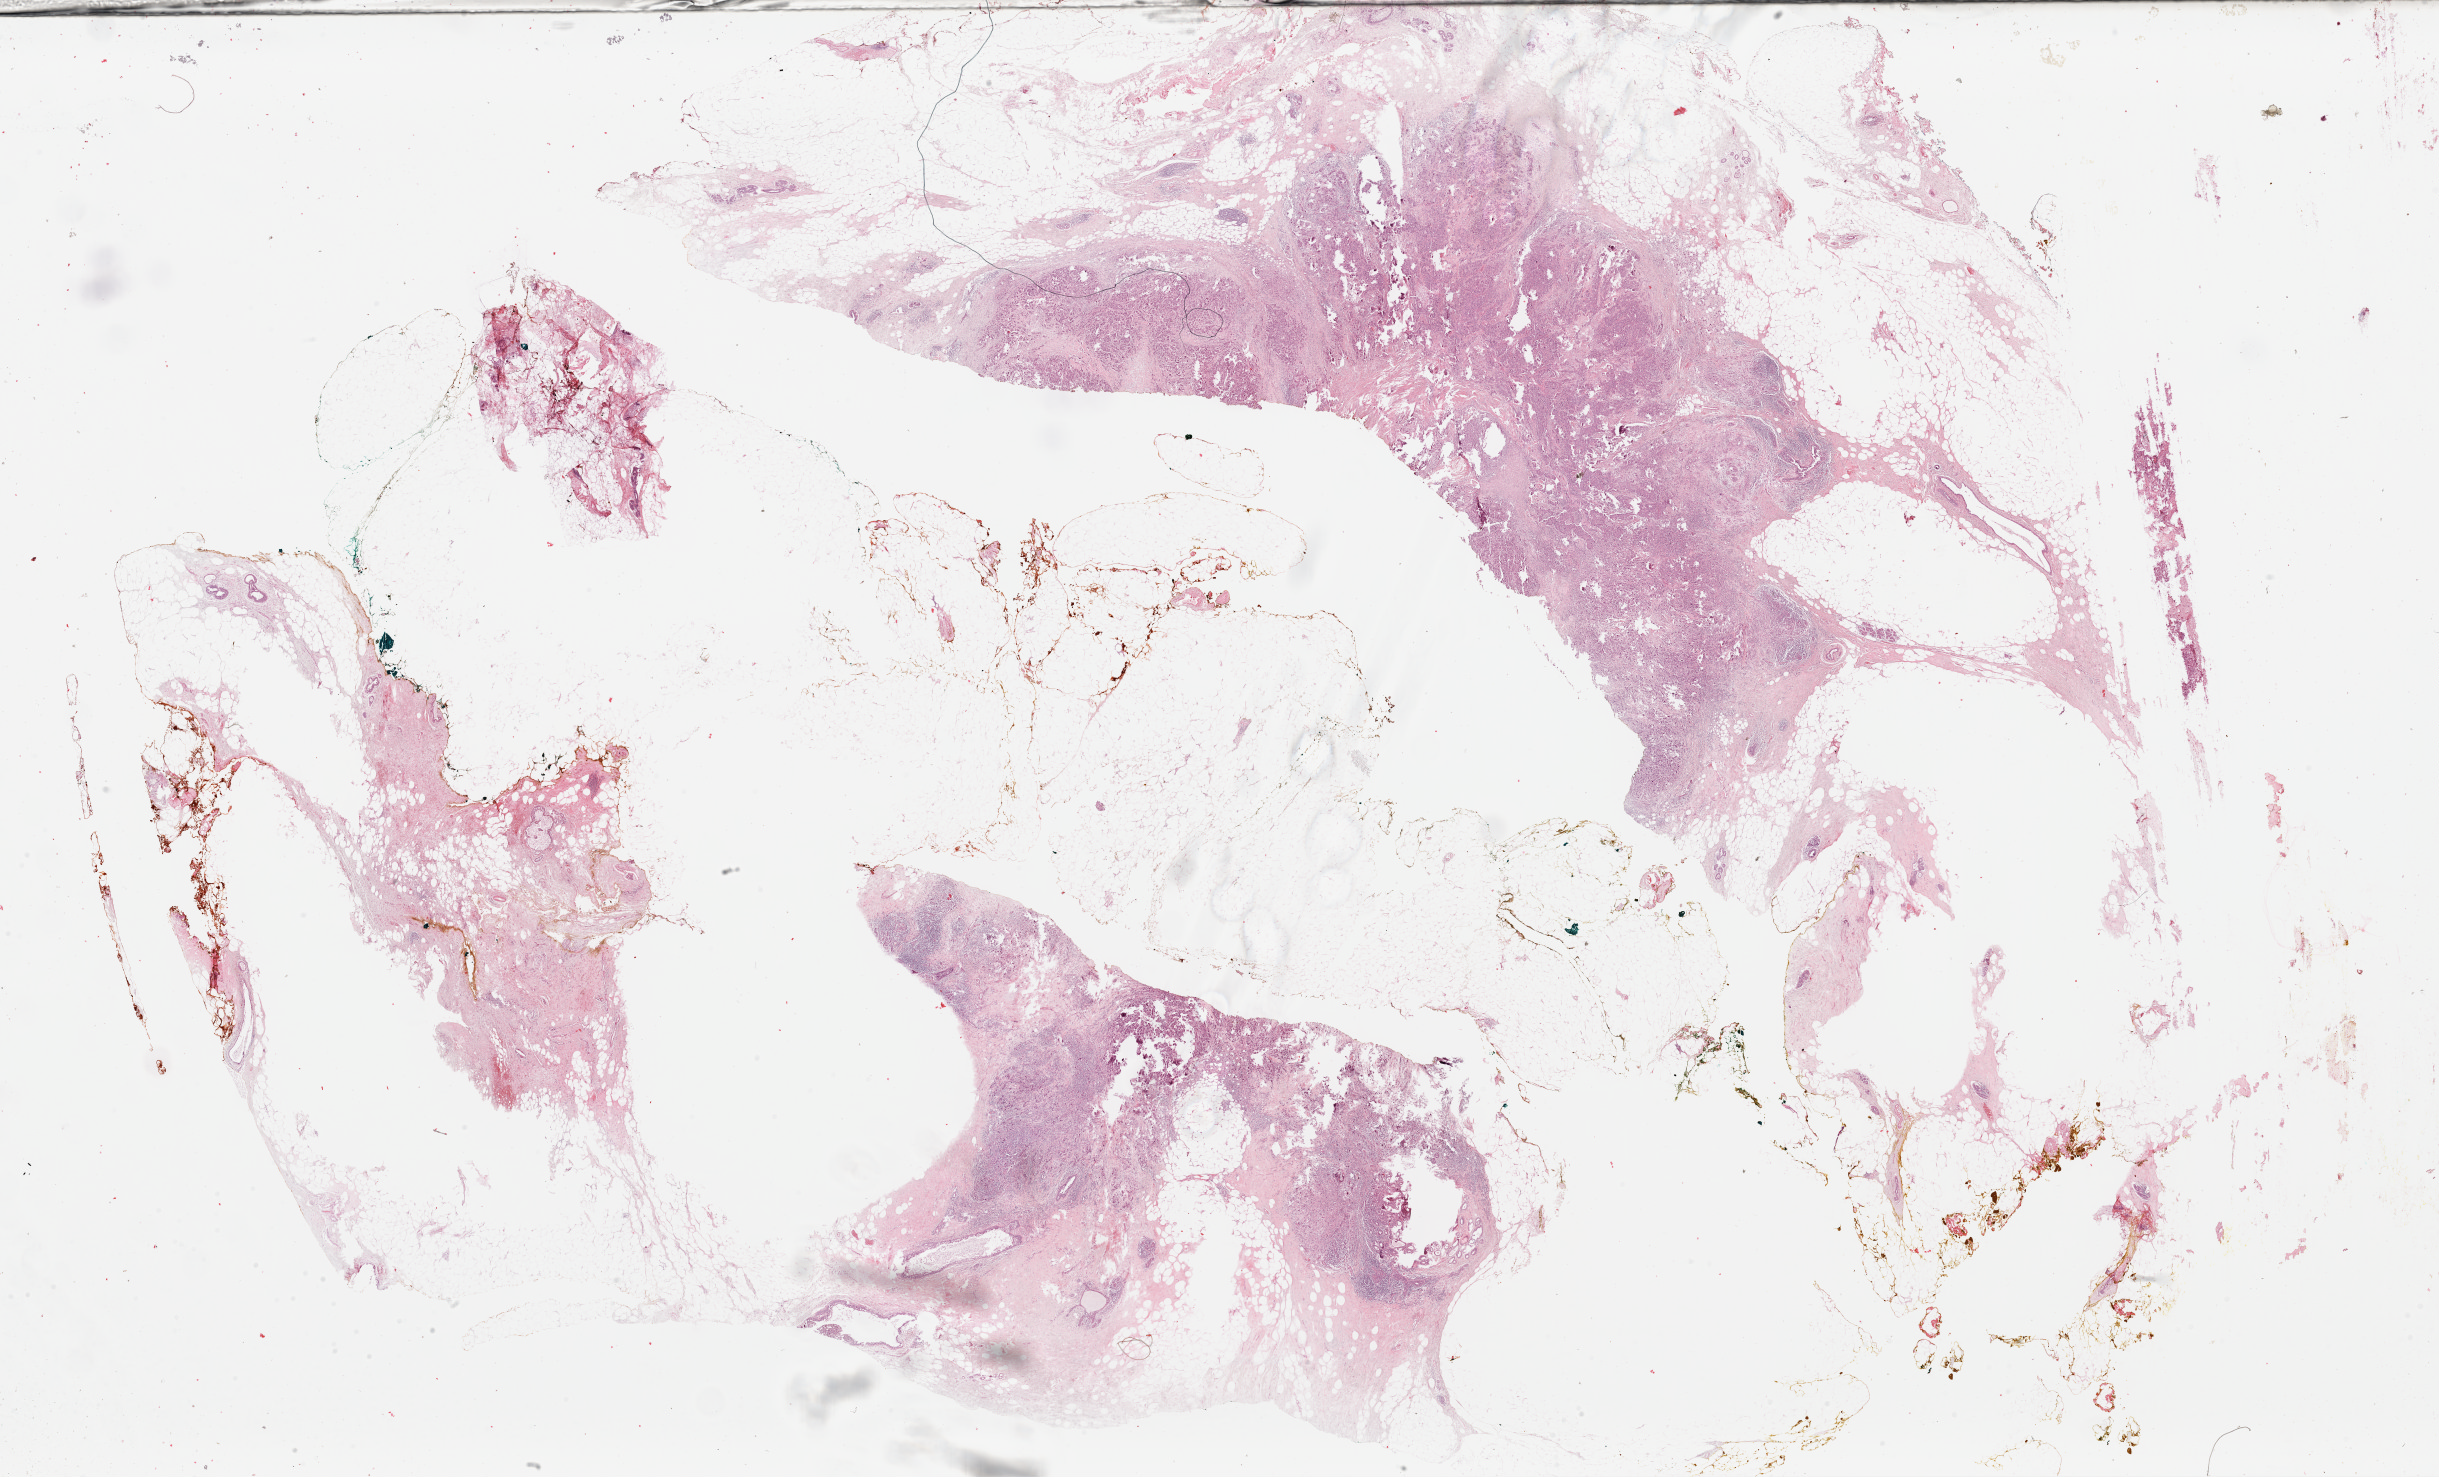
Digitized H&E tissue section (whole slide) — whole scanned area (about 38.5 x 23.3 mm, acquisition: 40x scan) shown as a low-resolution overview, formalin-fixed paraffin-embedded (FFPE) diagnostic section, breast, primary tumour sample. Female, age 66 years at initial diagnosis.
• laterality: right
• AJCC pathologic stage: IIA (7th edition)
• histologic diagnosis: Infiltrating duct carcinoma, NOS